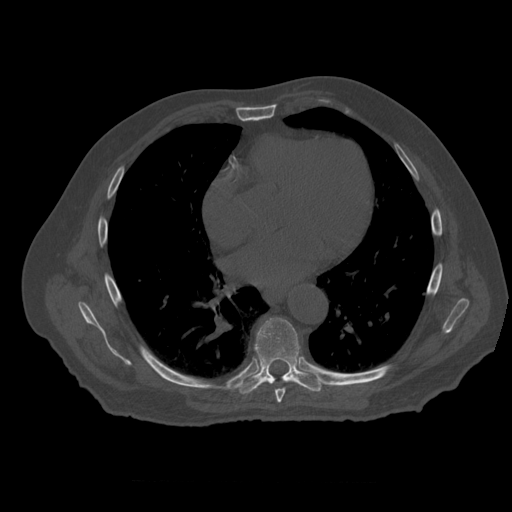
CT including the spine, one axial slice; reconstruction kernel STANDARD; 120 kVp; bone window (W 1800 / L 400 HU); 1.25 mm slice thickness; 512 × 512 image matrix. Patient age 73 years. From the clinical record (not read from this slice): primary cancer: prostate.
Outlined on this slice (semi-automatic segmentation, software-assisted and operator-edited):
- T7 vertebra: bounding box <275,389,286,403> (left, top, right, bottom; pixels)
- T8 vertebra: <239,318,323,395>